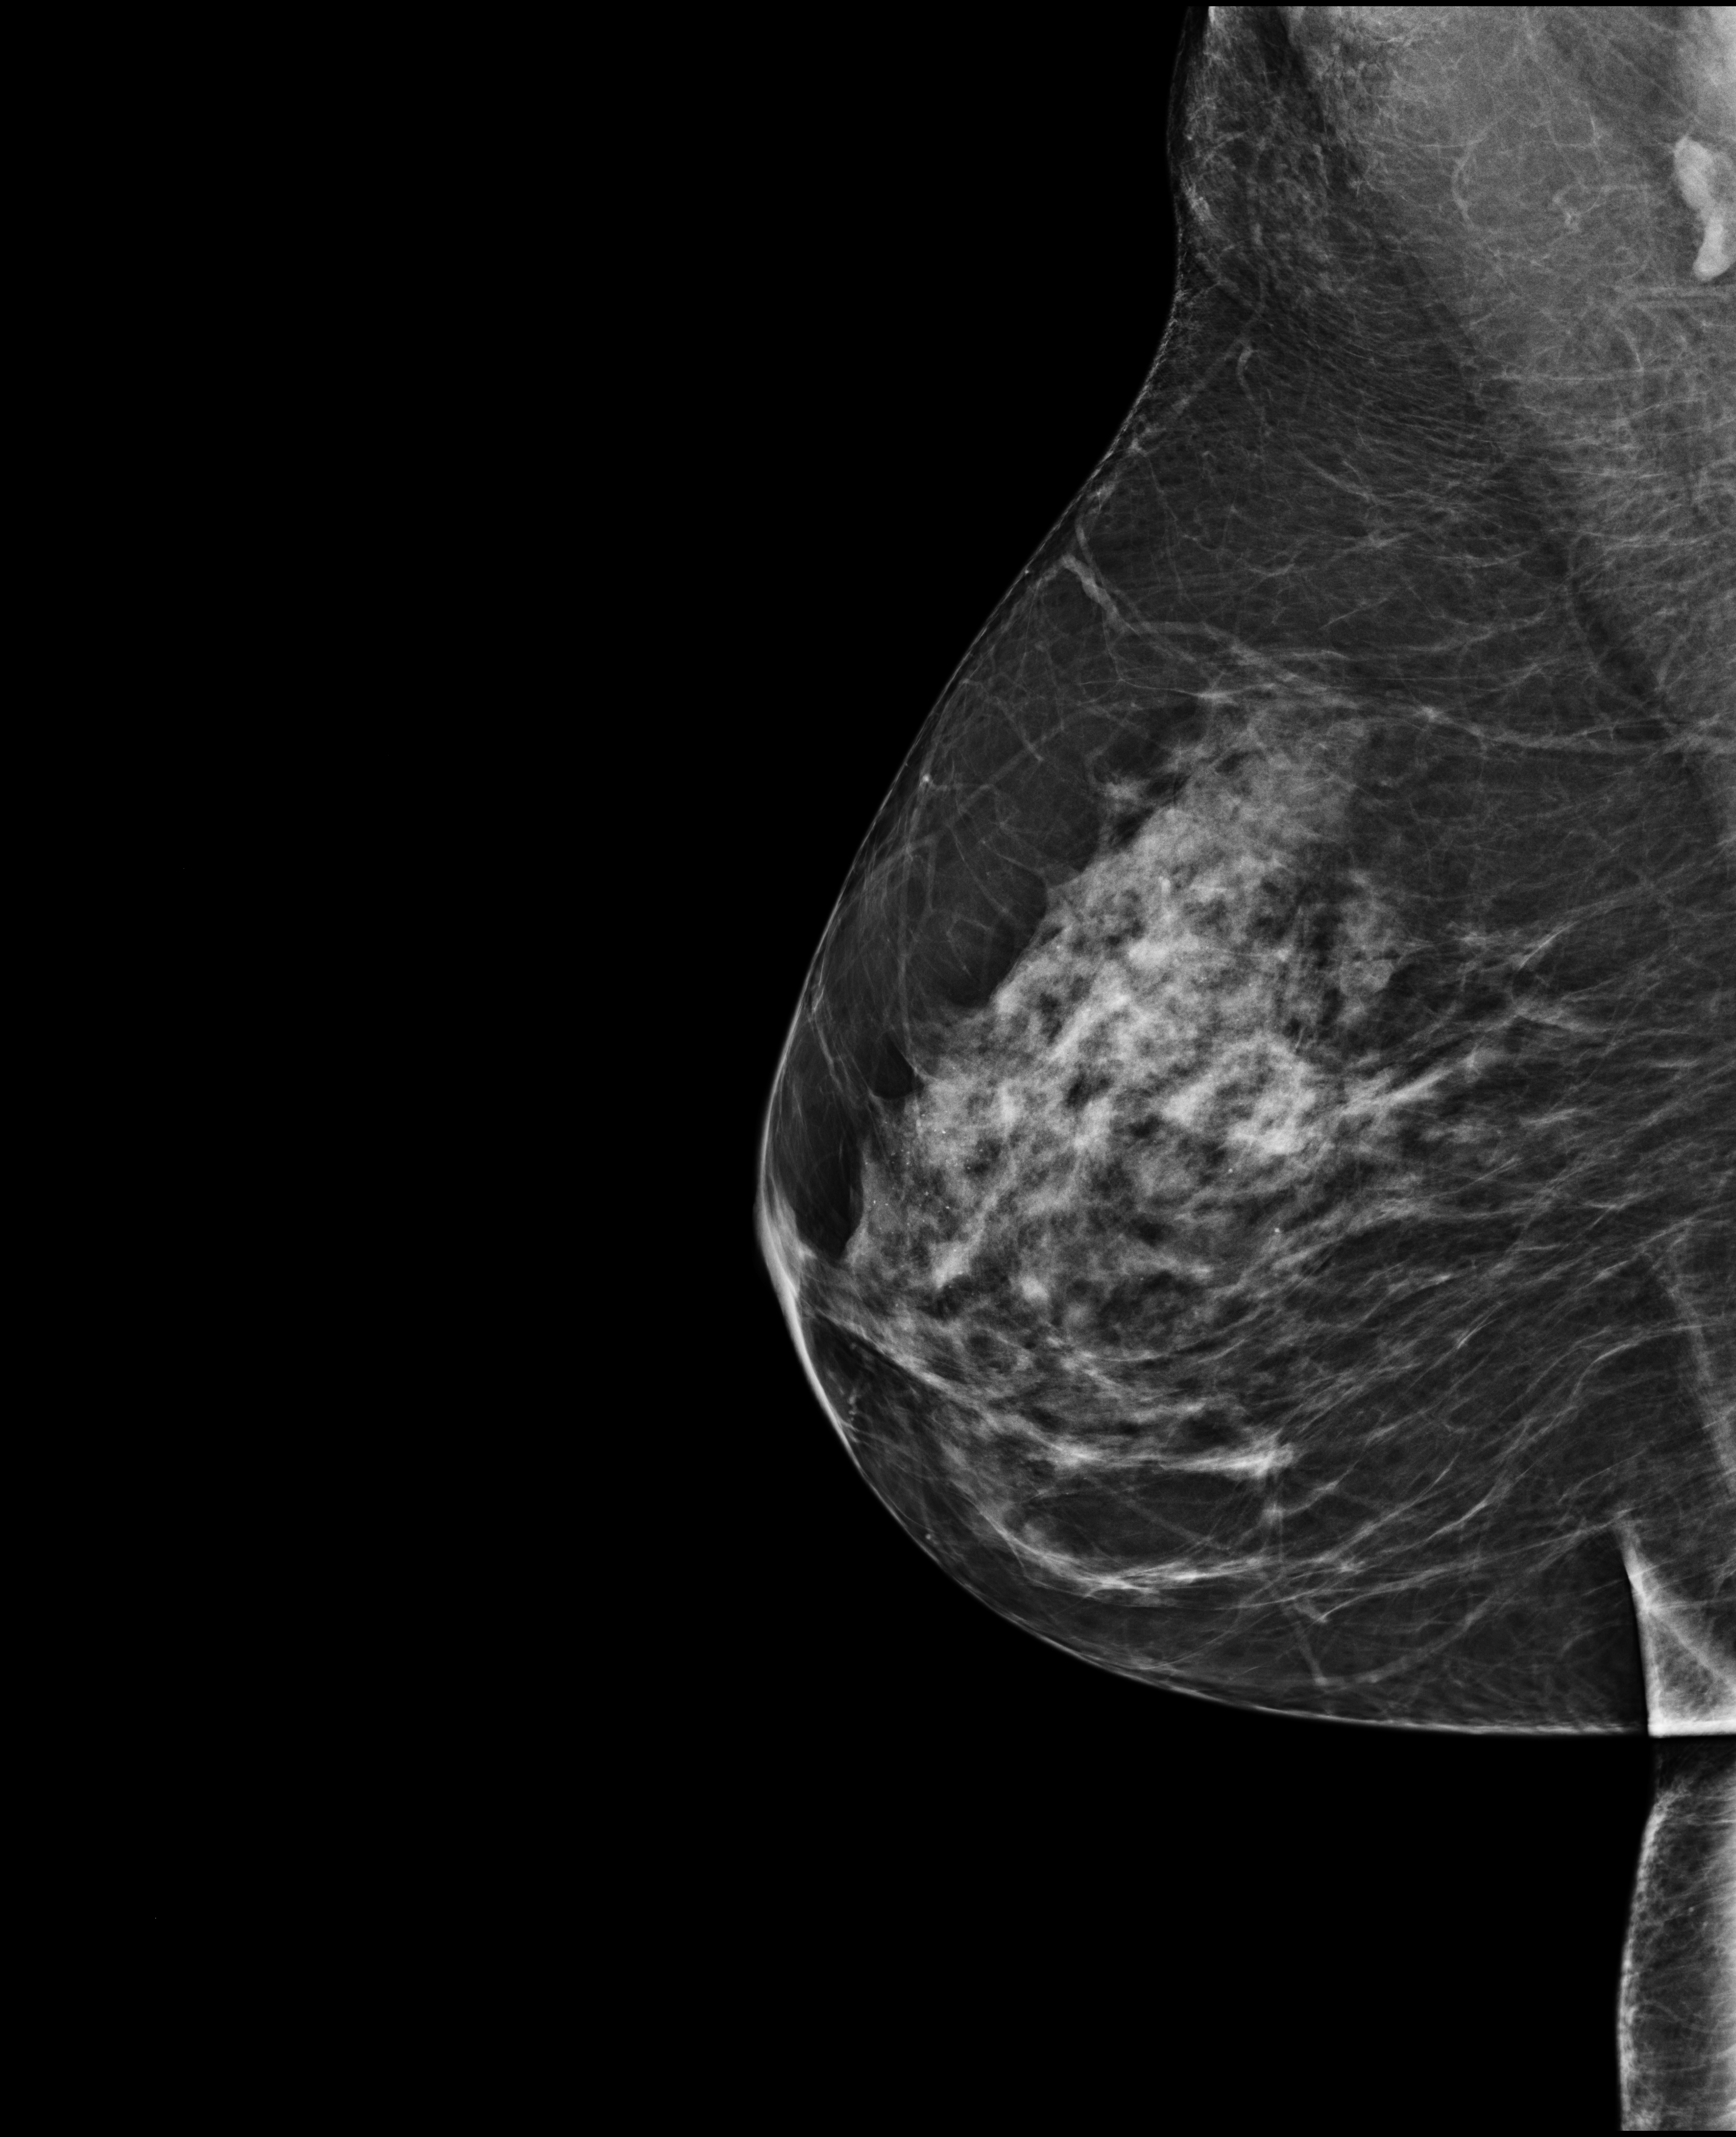
Full-field digital mammogram (FFDM); right breast; mediolateral oblique (MLO) view; screening examination. Female patient, age 49 years.
Final BI-RADS assessment for this screening round (tomosynthesis exam, both breasts): category 2.